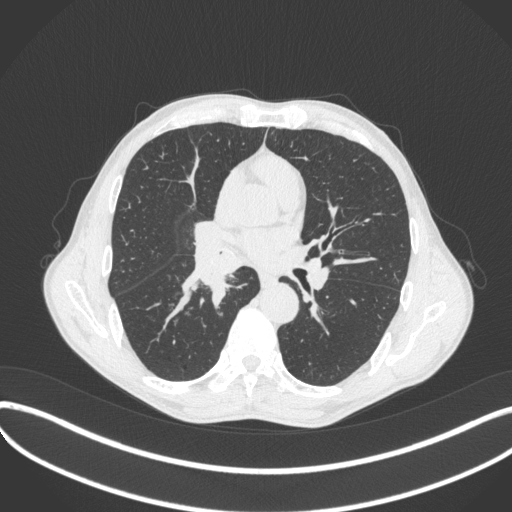
Chest CT, one axial slice; slice 231 of 481 in the series (ordered by position); reconstruction kernel B31f; 120 kVp; lung window (W 1500 / L -600 HU); 512 × 512 image matrix, field of view 400 × 400 mm. Patient: male, 65 years. Case-level facts recorded for this patient, not image findings: clinical TNM (as recorded): T2a N0 M0.
Outlined on this slice (bounding box drawn by a radiologist):
- lung tumour (recorded histology: squamous cell carcinoma): box from (x=185, y=236) to (x=248, y=318) px